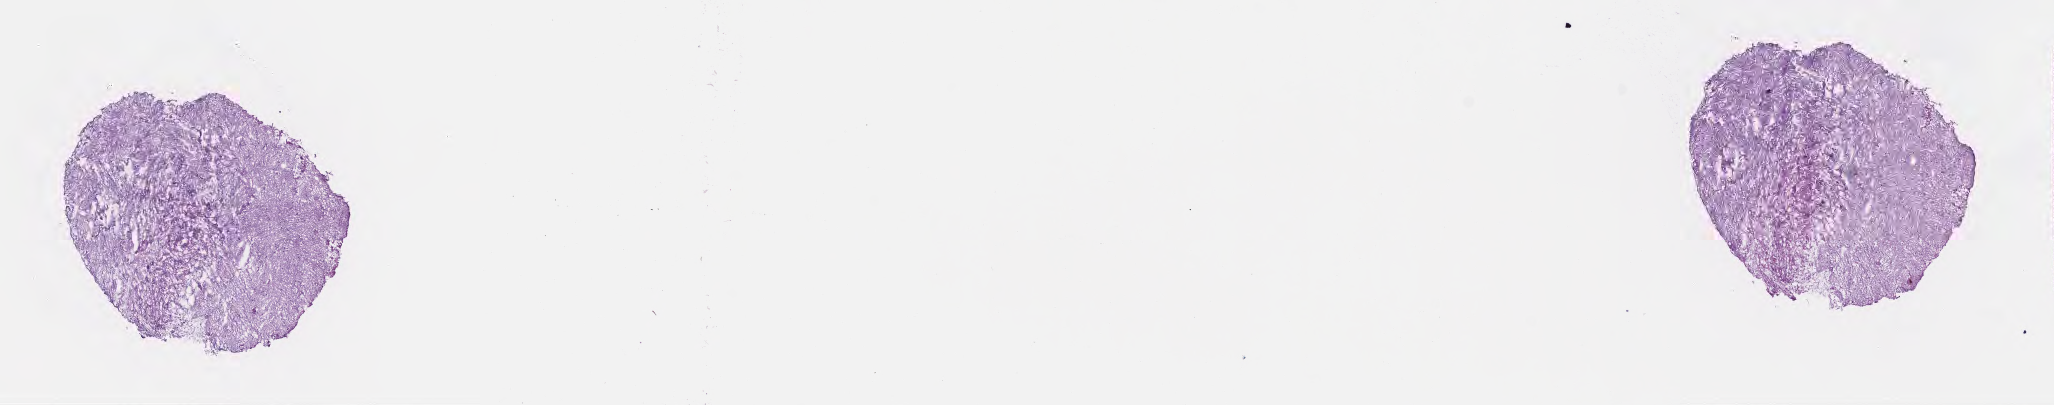
Digitized H&E-stained section — a low-resolution overview of the entire scanned area, about 16.6 x 3.3 mm, frozen section (tissue freezing medium), specimen: recurrent tumor, anatomic site: brain. Female patient; age at initial diagnosis 63 years. Pathologist review of this section (percent, as recorded): tumor cells 20%, tumor nuclei 43%, stromal cells 54%, necrosis 0%, normal cells 26%. Inflammatory infiltration, as recorded: lymphocyte infiltration 0%, monocyte infiltration 1%, neutrophil infiltration 0%.
Patient diagnosis: Glioblastoma, NOS. Section: top of the tissue portion.